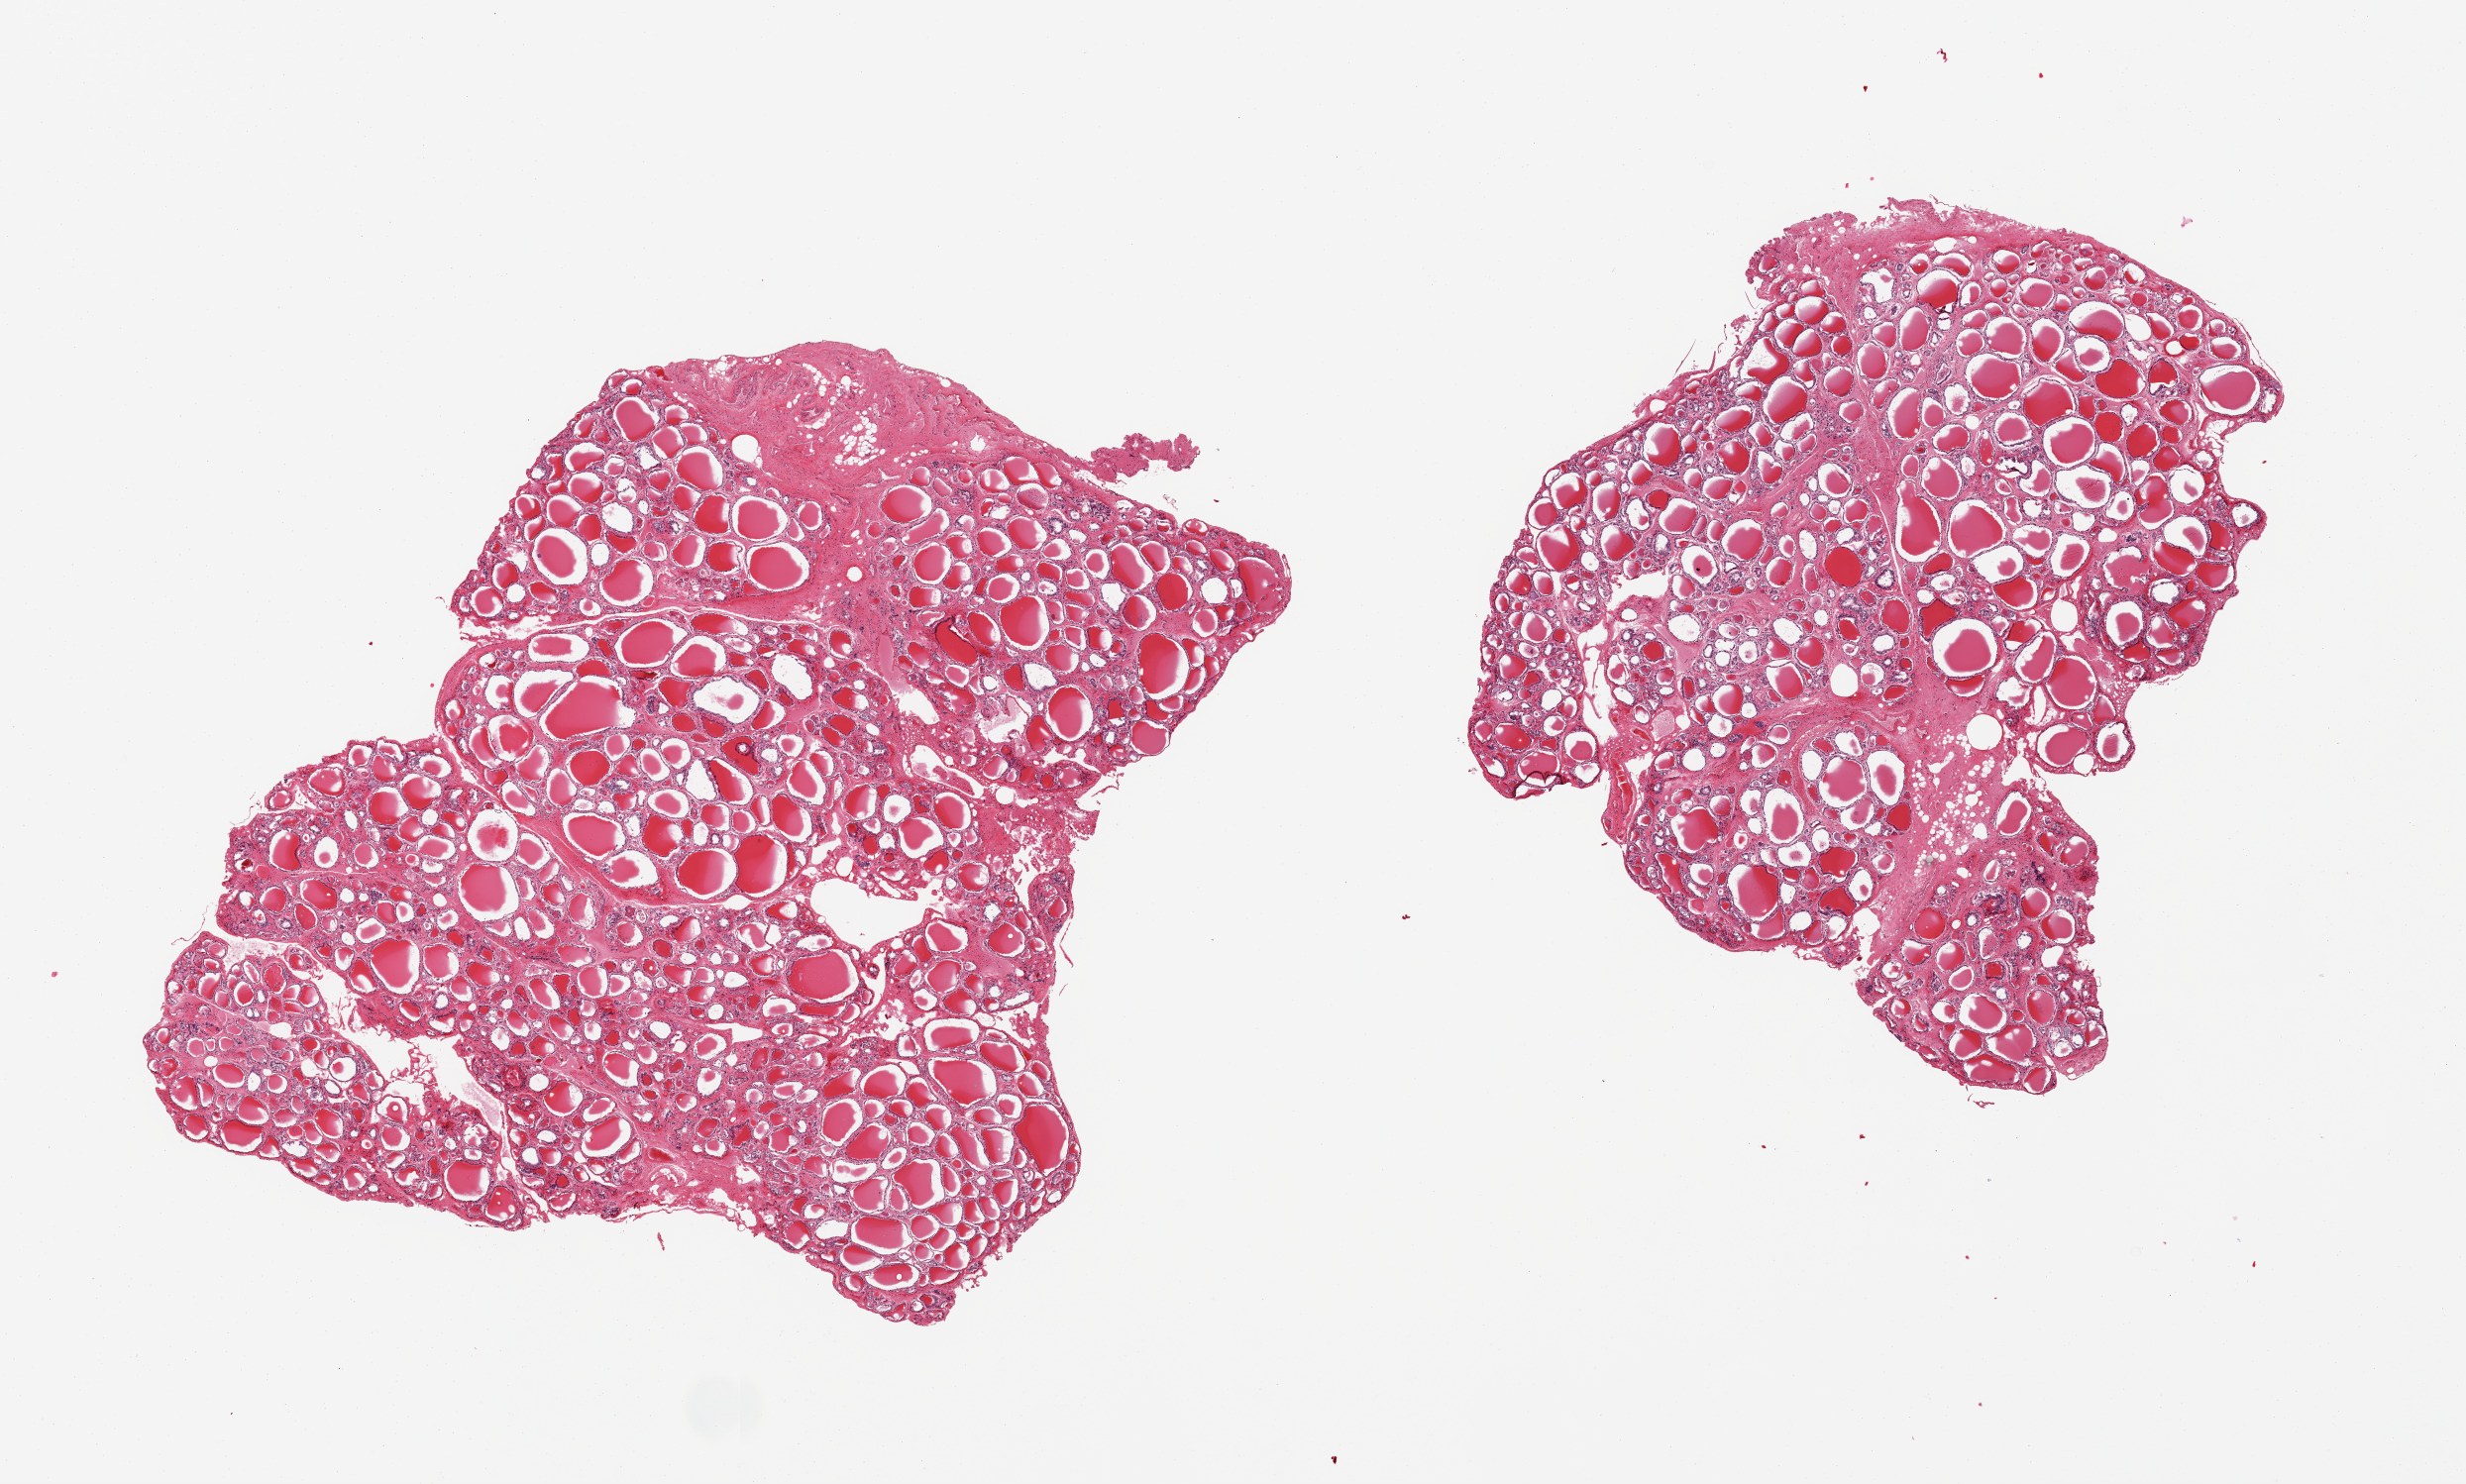
Haematoxylin and eosin whole-slide image, a low-resolution overview of the entire scanned area, about 19.7 x 11.8 mm. PAXgene-fixed paraffin-embedded (PFPE) section. Sampled site (target tissue): thyroid. Tissue donor sample. Donor: male.
* reviewer comment on this tissue sample: 2 pieces